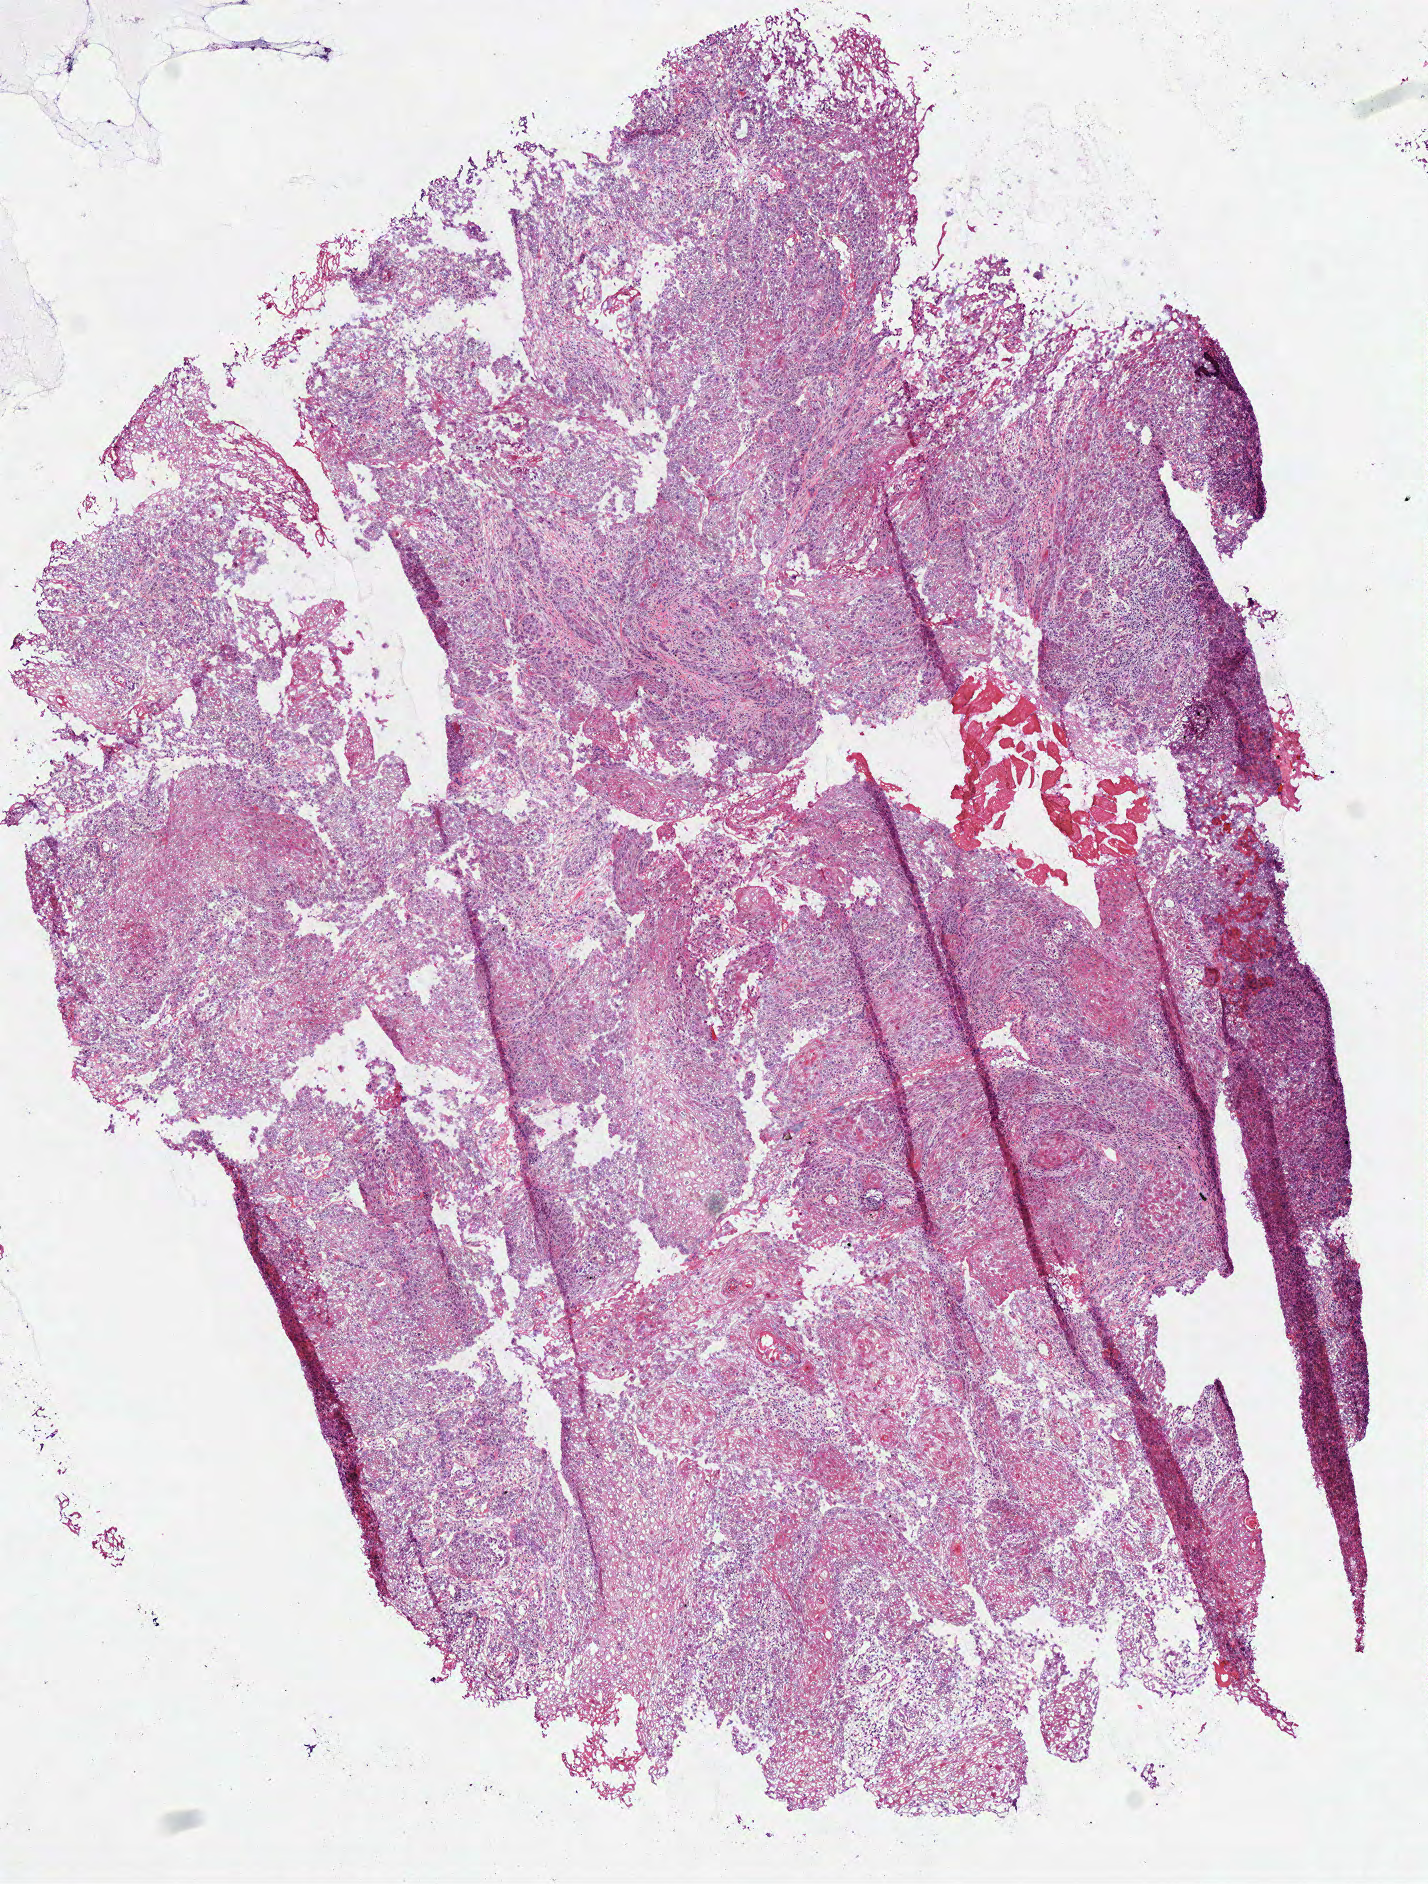
Whole-slide histology image, Hematoxylin and eosin (H&E) stained, shown as a low-resolution overview of the whole scanned area (about 5.6 x 7.4 mm, slide scanned at 40x). Frozen section. Primary tumour sample from the head and neck. Patient: male, age at initial diagnosis 47 years. Histologic grade: G2 (moderately differentiated). Slide review estimates, as recorded: tumour cells 95%, tumour nuclei 98%, normal cells 0%, stromal cells 4%, necrosis 1%. Inflammatory infiltration, as recorded: lymphocyte infiltration 1%.
Pathologic diagnosis: Squamous cell carcinoma, NOS (floor of mouth, NOS).